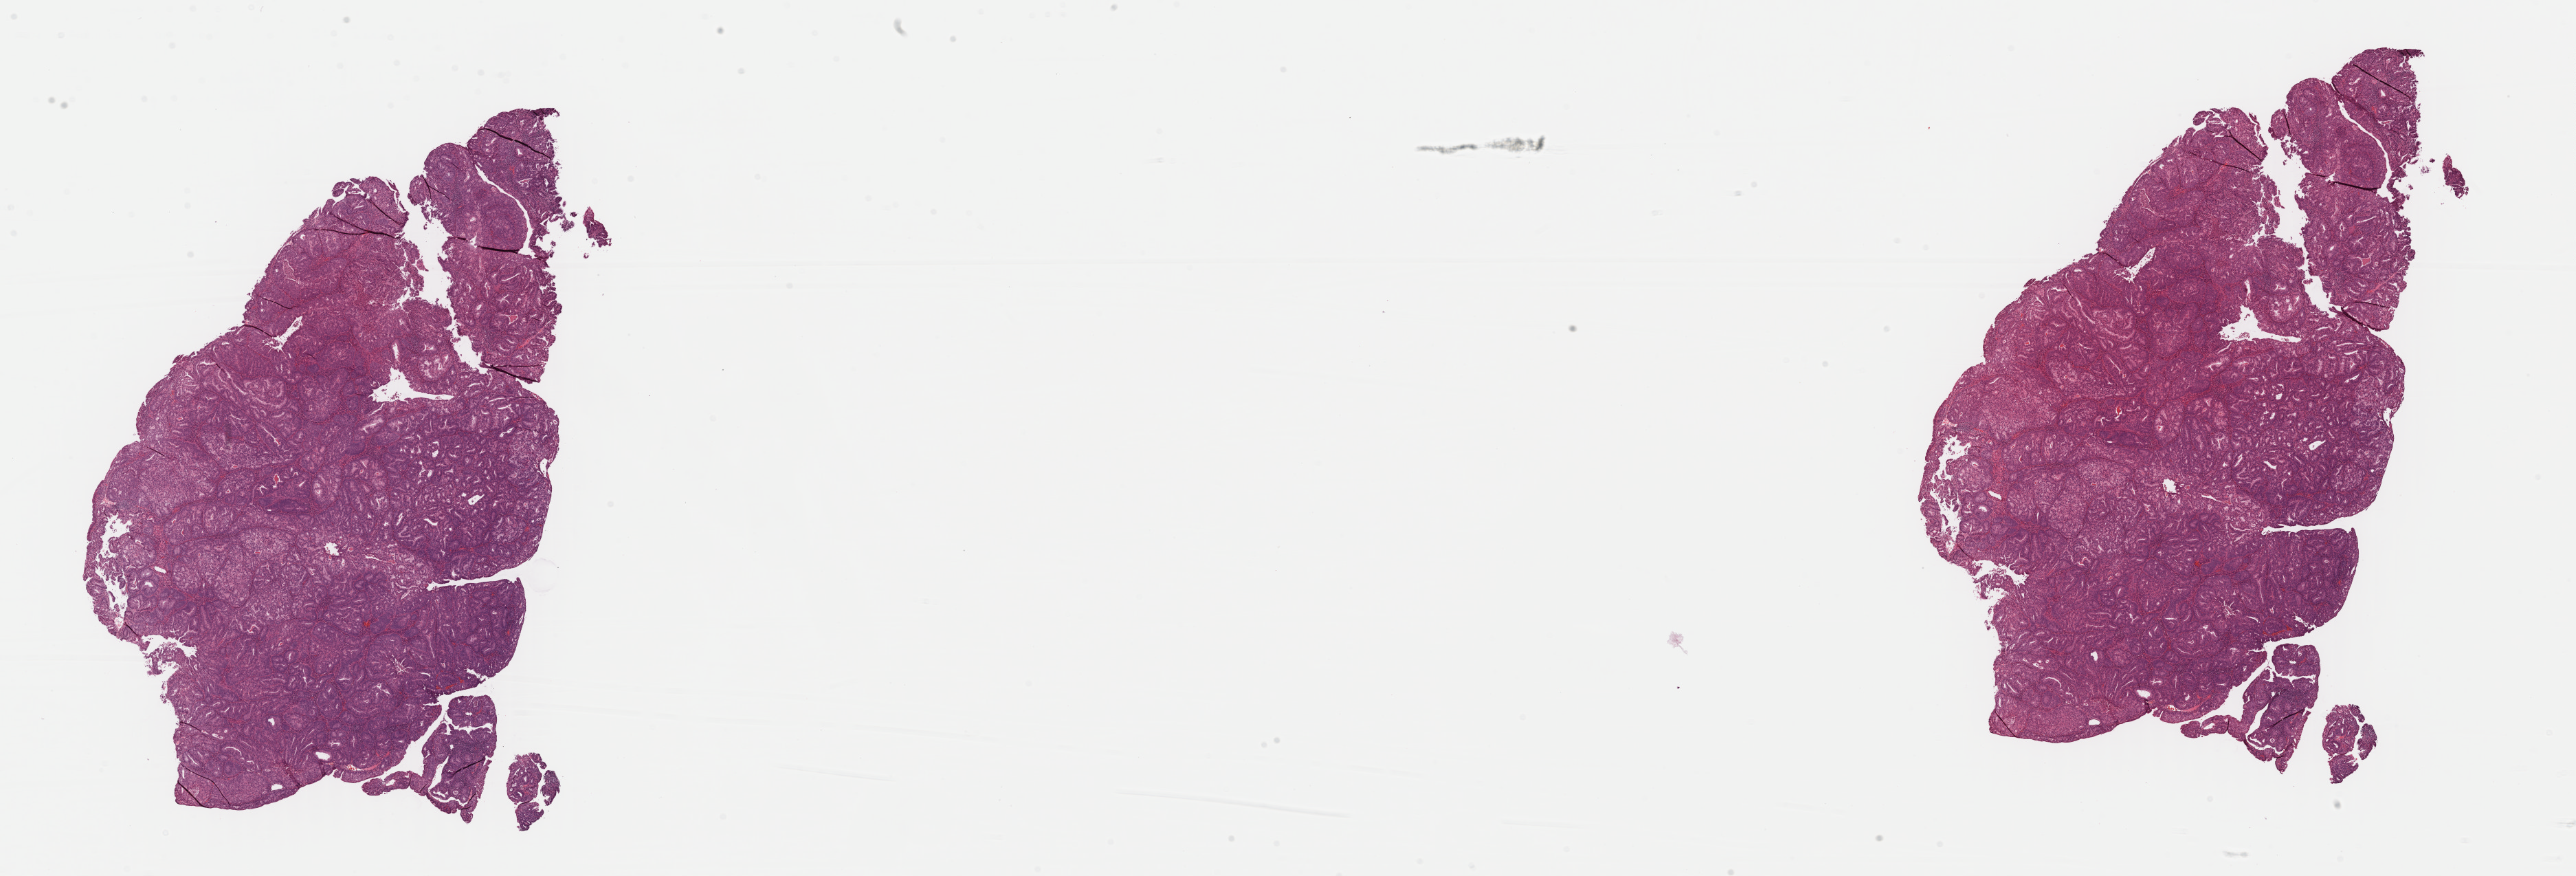
Whole-slide histology image, H&E, a low-resolution overview of the entire scanned area, about 29.6 x 10.1 mm; formalin-fixed paraffin-embedded (FFPE) diagnostic section; primary tumour sample from the uterus. Female, age 57 years at initial diagnosis. Histologic grade: G1 (well differentiated).
• diagnosis: Endometrioid adenocarcinoma, NOS (endometrium)
• FIGO stage: IB